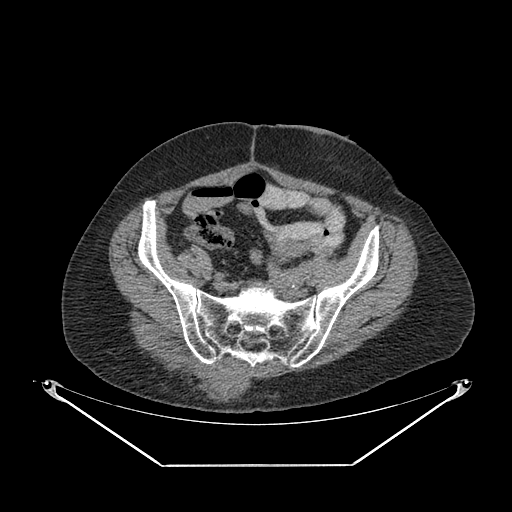
CT of an extremity soft-tissue mass (from a PET/CT study), one axial slice; position 74 of 267 along the scan axis; soft-tissue window (W 400 / L 40 HU); 3.75 mm slice thickness; 512 × 512 image matrix, field of view 500 × 500 mm. Female patient. From the clinical record (not read from this slice): histological type: spindle cell suggestive of myxofibrosarcoma; grade: intermediate; site of the primary tumour: right buttock.
Annotated regions visible in this slice (expert contour drawn on MRI and transferred to this co-registered scan by the dataset authors):
- gross tumour volume (mass): bounding box (x1, y1, x2, y2) in pixels: (148, 358, 250, 405)